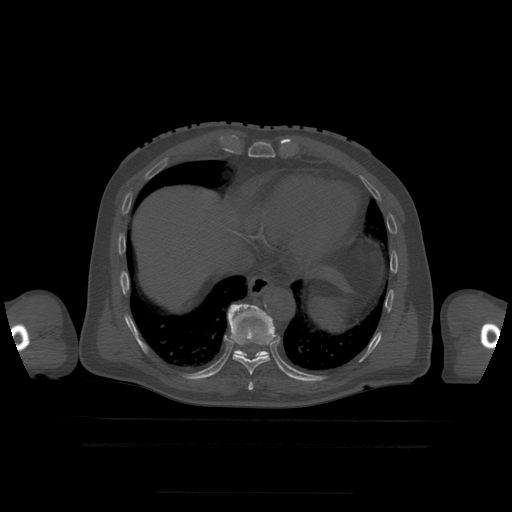
CT including the spine, one axial slice. Bone window (W 1800 / L 400 HU). 512 × 512 image matrix. Patient age 68 years. Case-level facts recorded for this patient, not image findings: primary cancer: urothelial.
Outlined on this slice (semi-automatically segmented with operator editing):
- T10 vertebra: box from (x=227, y=304) to (x=269, y=357) px
- T8 vertebra: (x=249, y=382)–(x=254, y=391)
- T9 vertebra: (x=229, y=305)–(x=277, y=388)